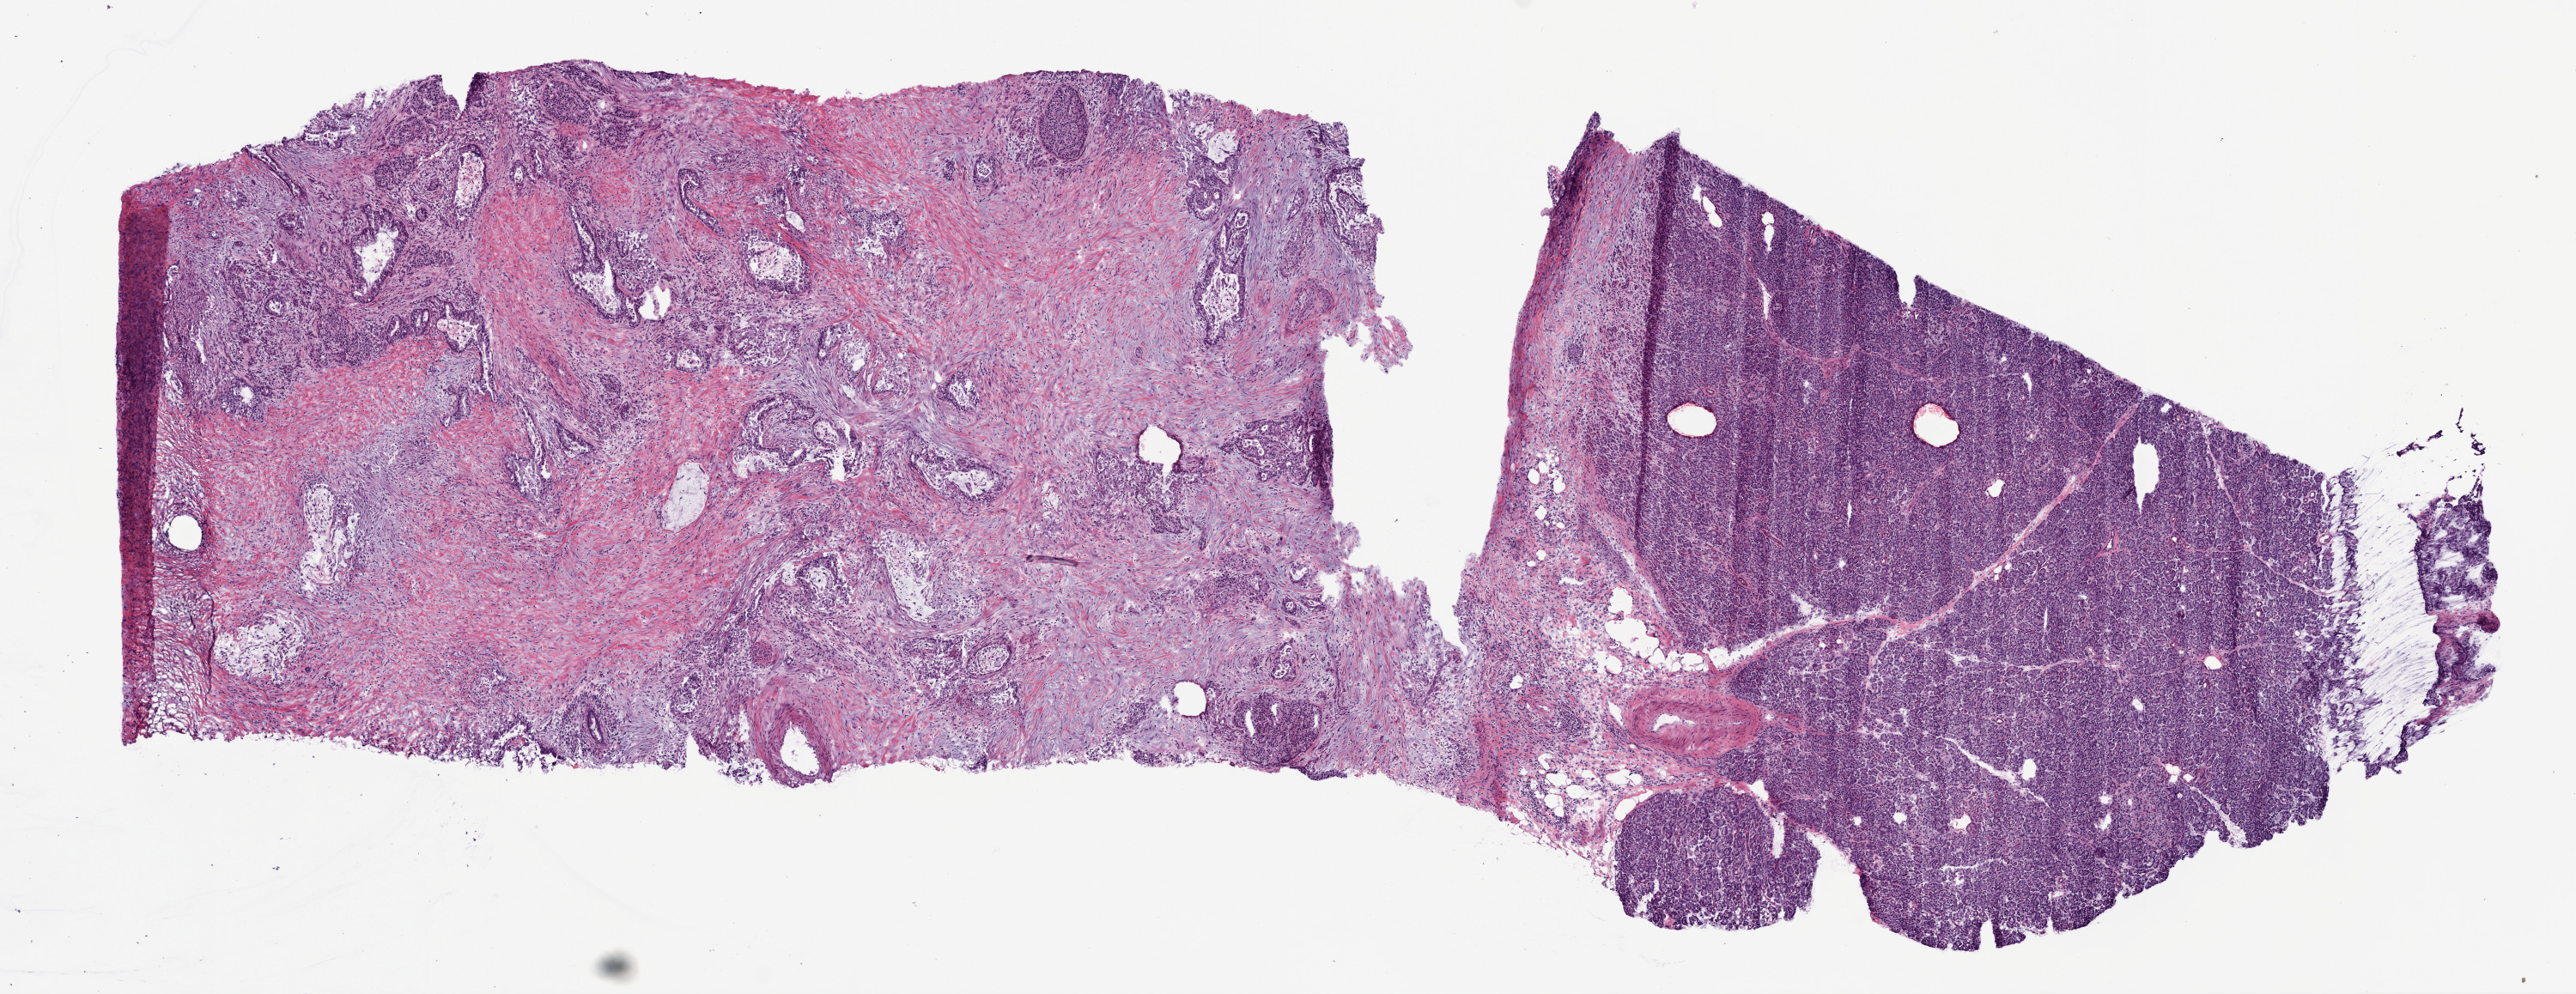
Whole-slide histology image, H&E, low-resolution overview of the scanned area, about 12.0 x 4.6 mm, frozen section, pancreas, primary tumour sample. Female, age 65 years at initial diagnosis. Histologic grade: G2 (moderately differentiated). Composition of this section per pathologist review: tumour cells 50%, tumour nuclei 25%, normal cells 40%, stromal cells 10%, necrosis 0%.
AJCC pathologic stage: IIB. Histologic diagnosis: Infiltrating duct carcinoma, NOS (head of pancreas). TNM: T3 N1 MX. Lymph nodes positive (case pathology): 1 of 12 examined.